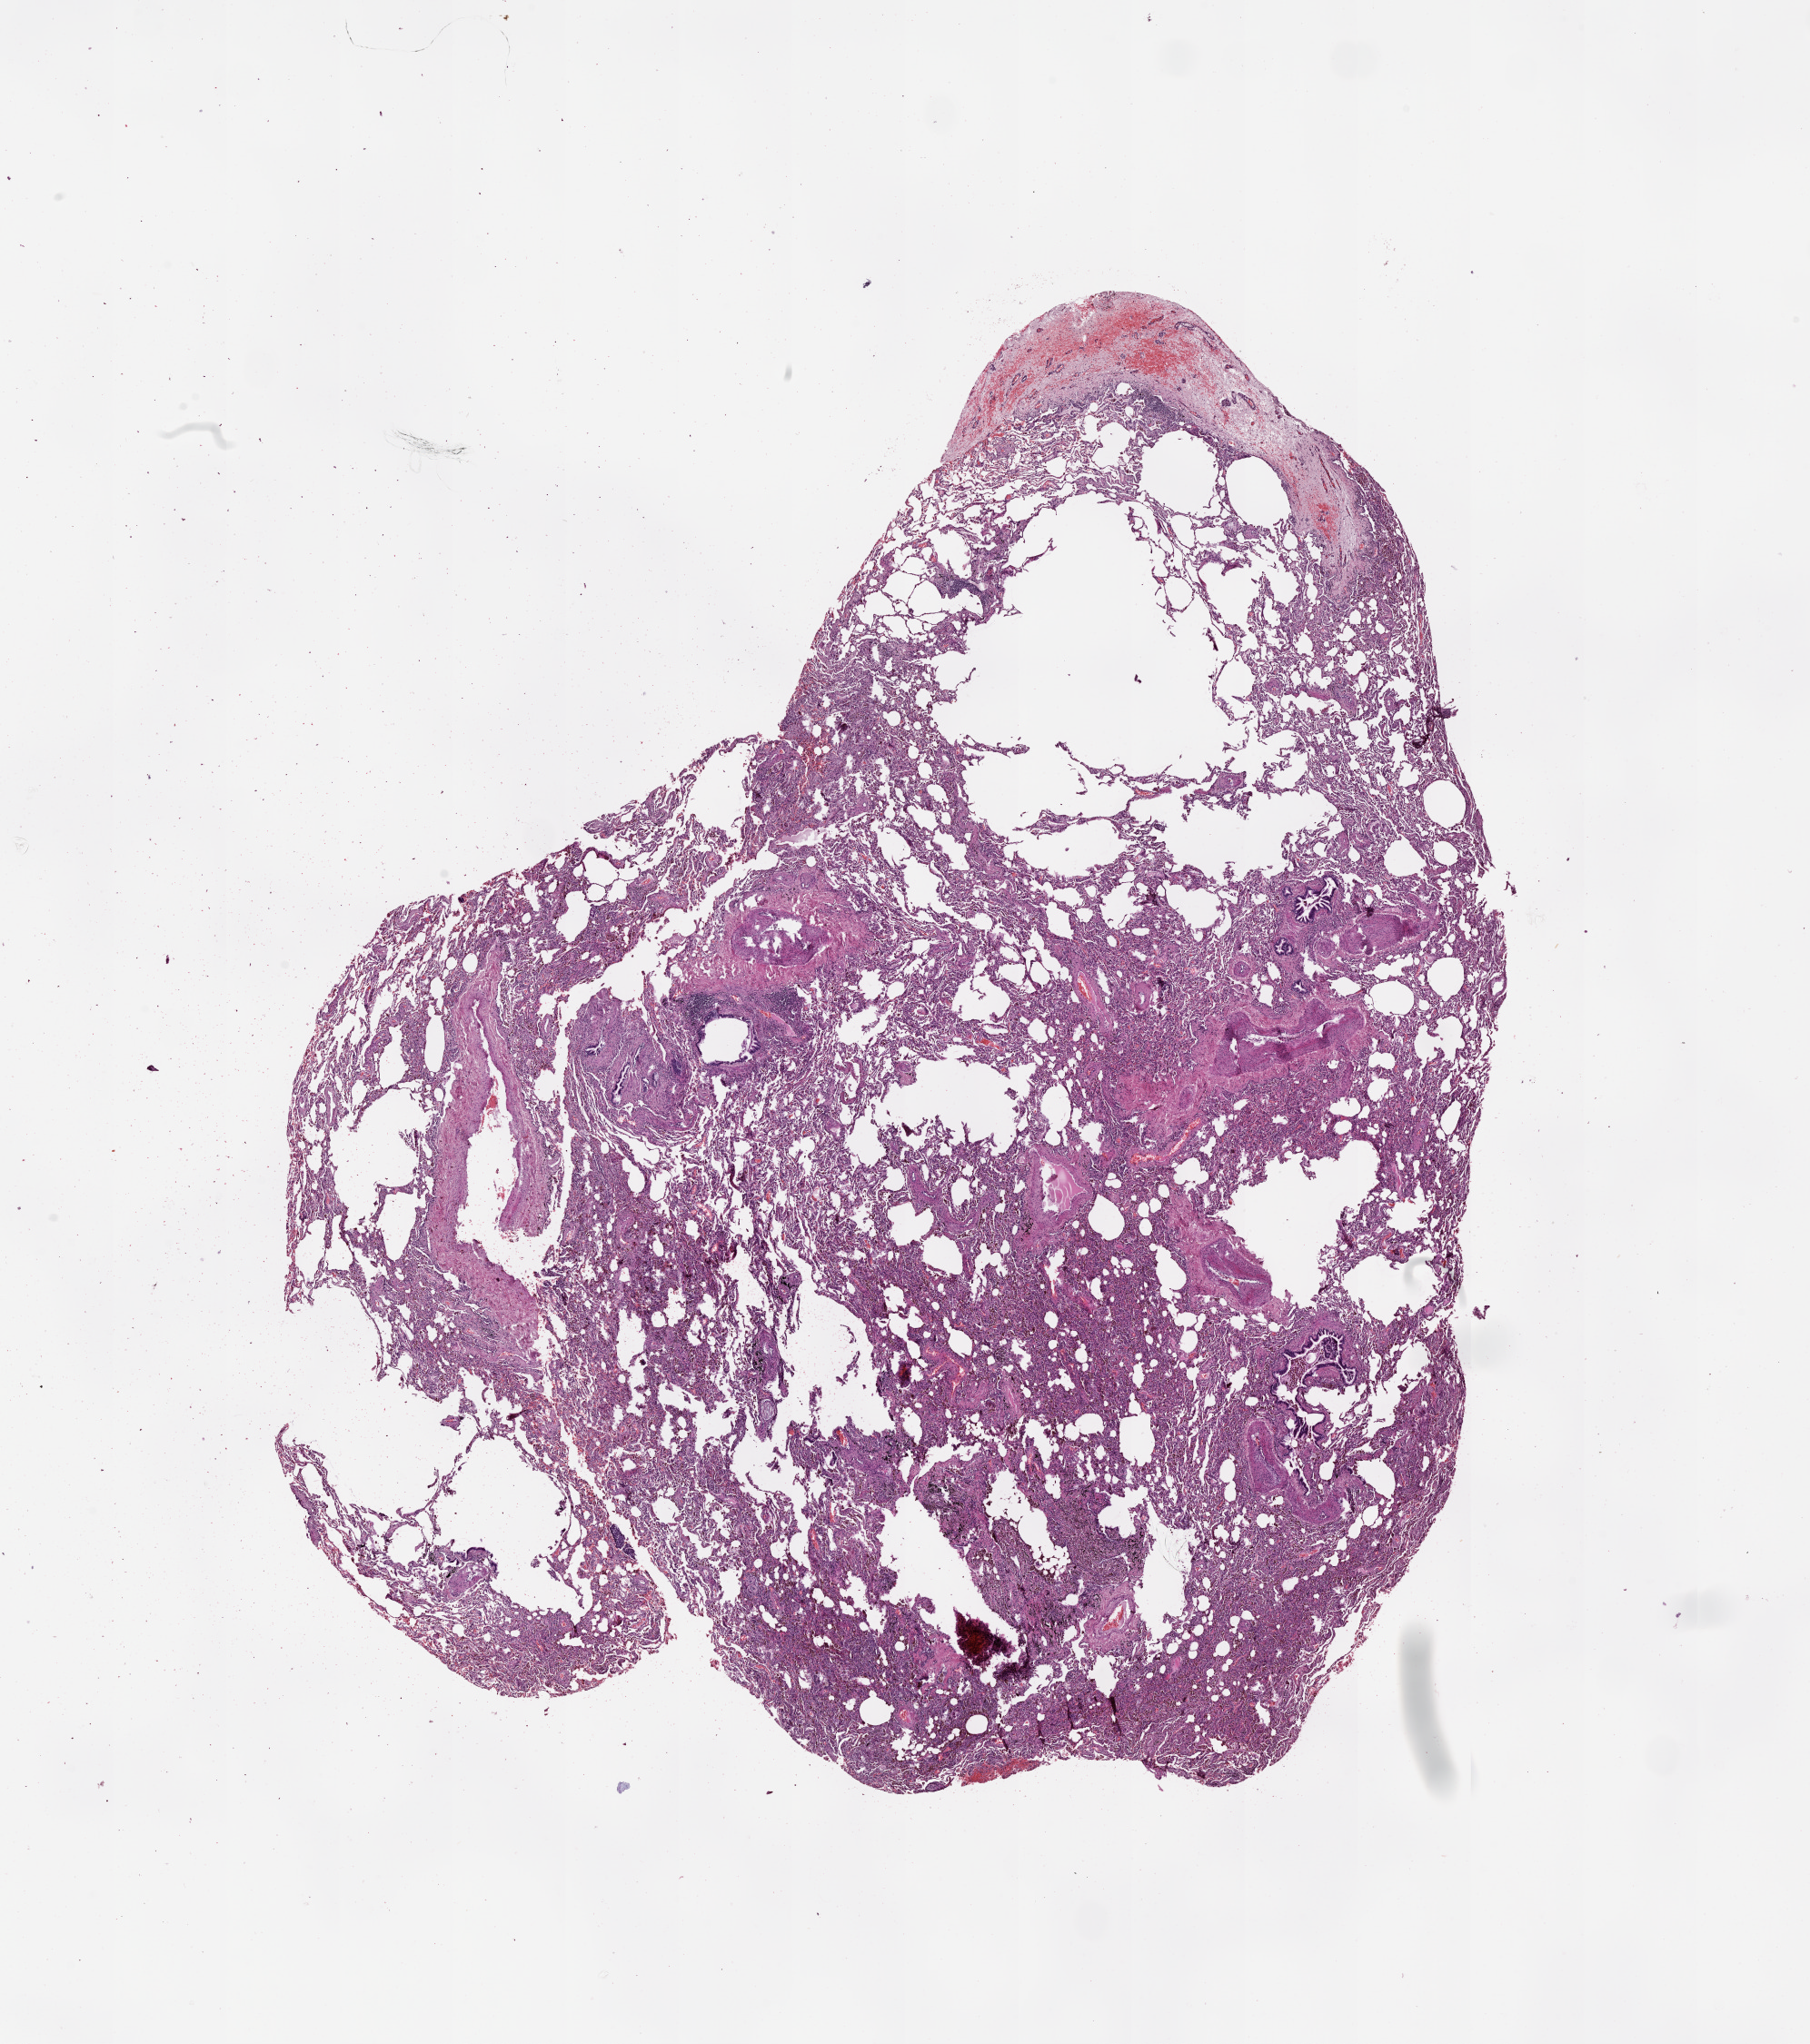
Digitized H&E-stained tissue section (whole slide), a low-resolution overview of the entire scanned area, about 16.0 x 18.1 mm (from a 20x scan), normal (non-tumour) tissue sample, lung. Patient: male, age 59 years.
- this section: normal (non-tumour) tissue from the same patient
- patient diagnosis (cohort enrolment): squamous cell carcinoma (lung)